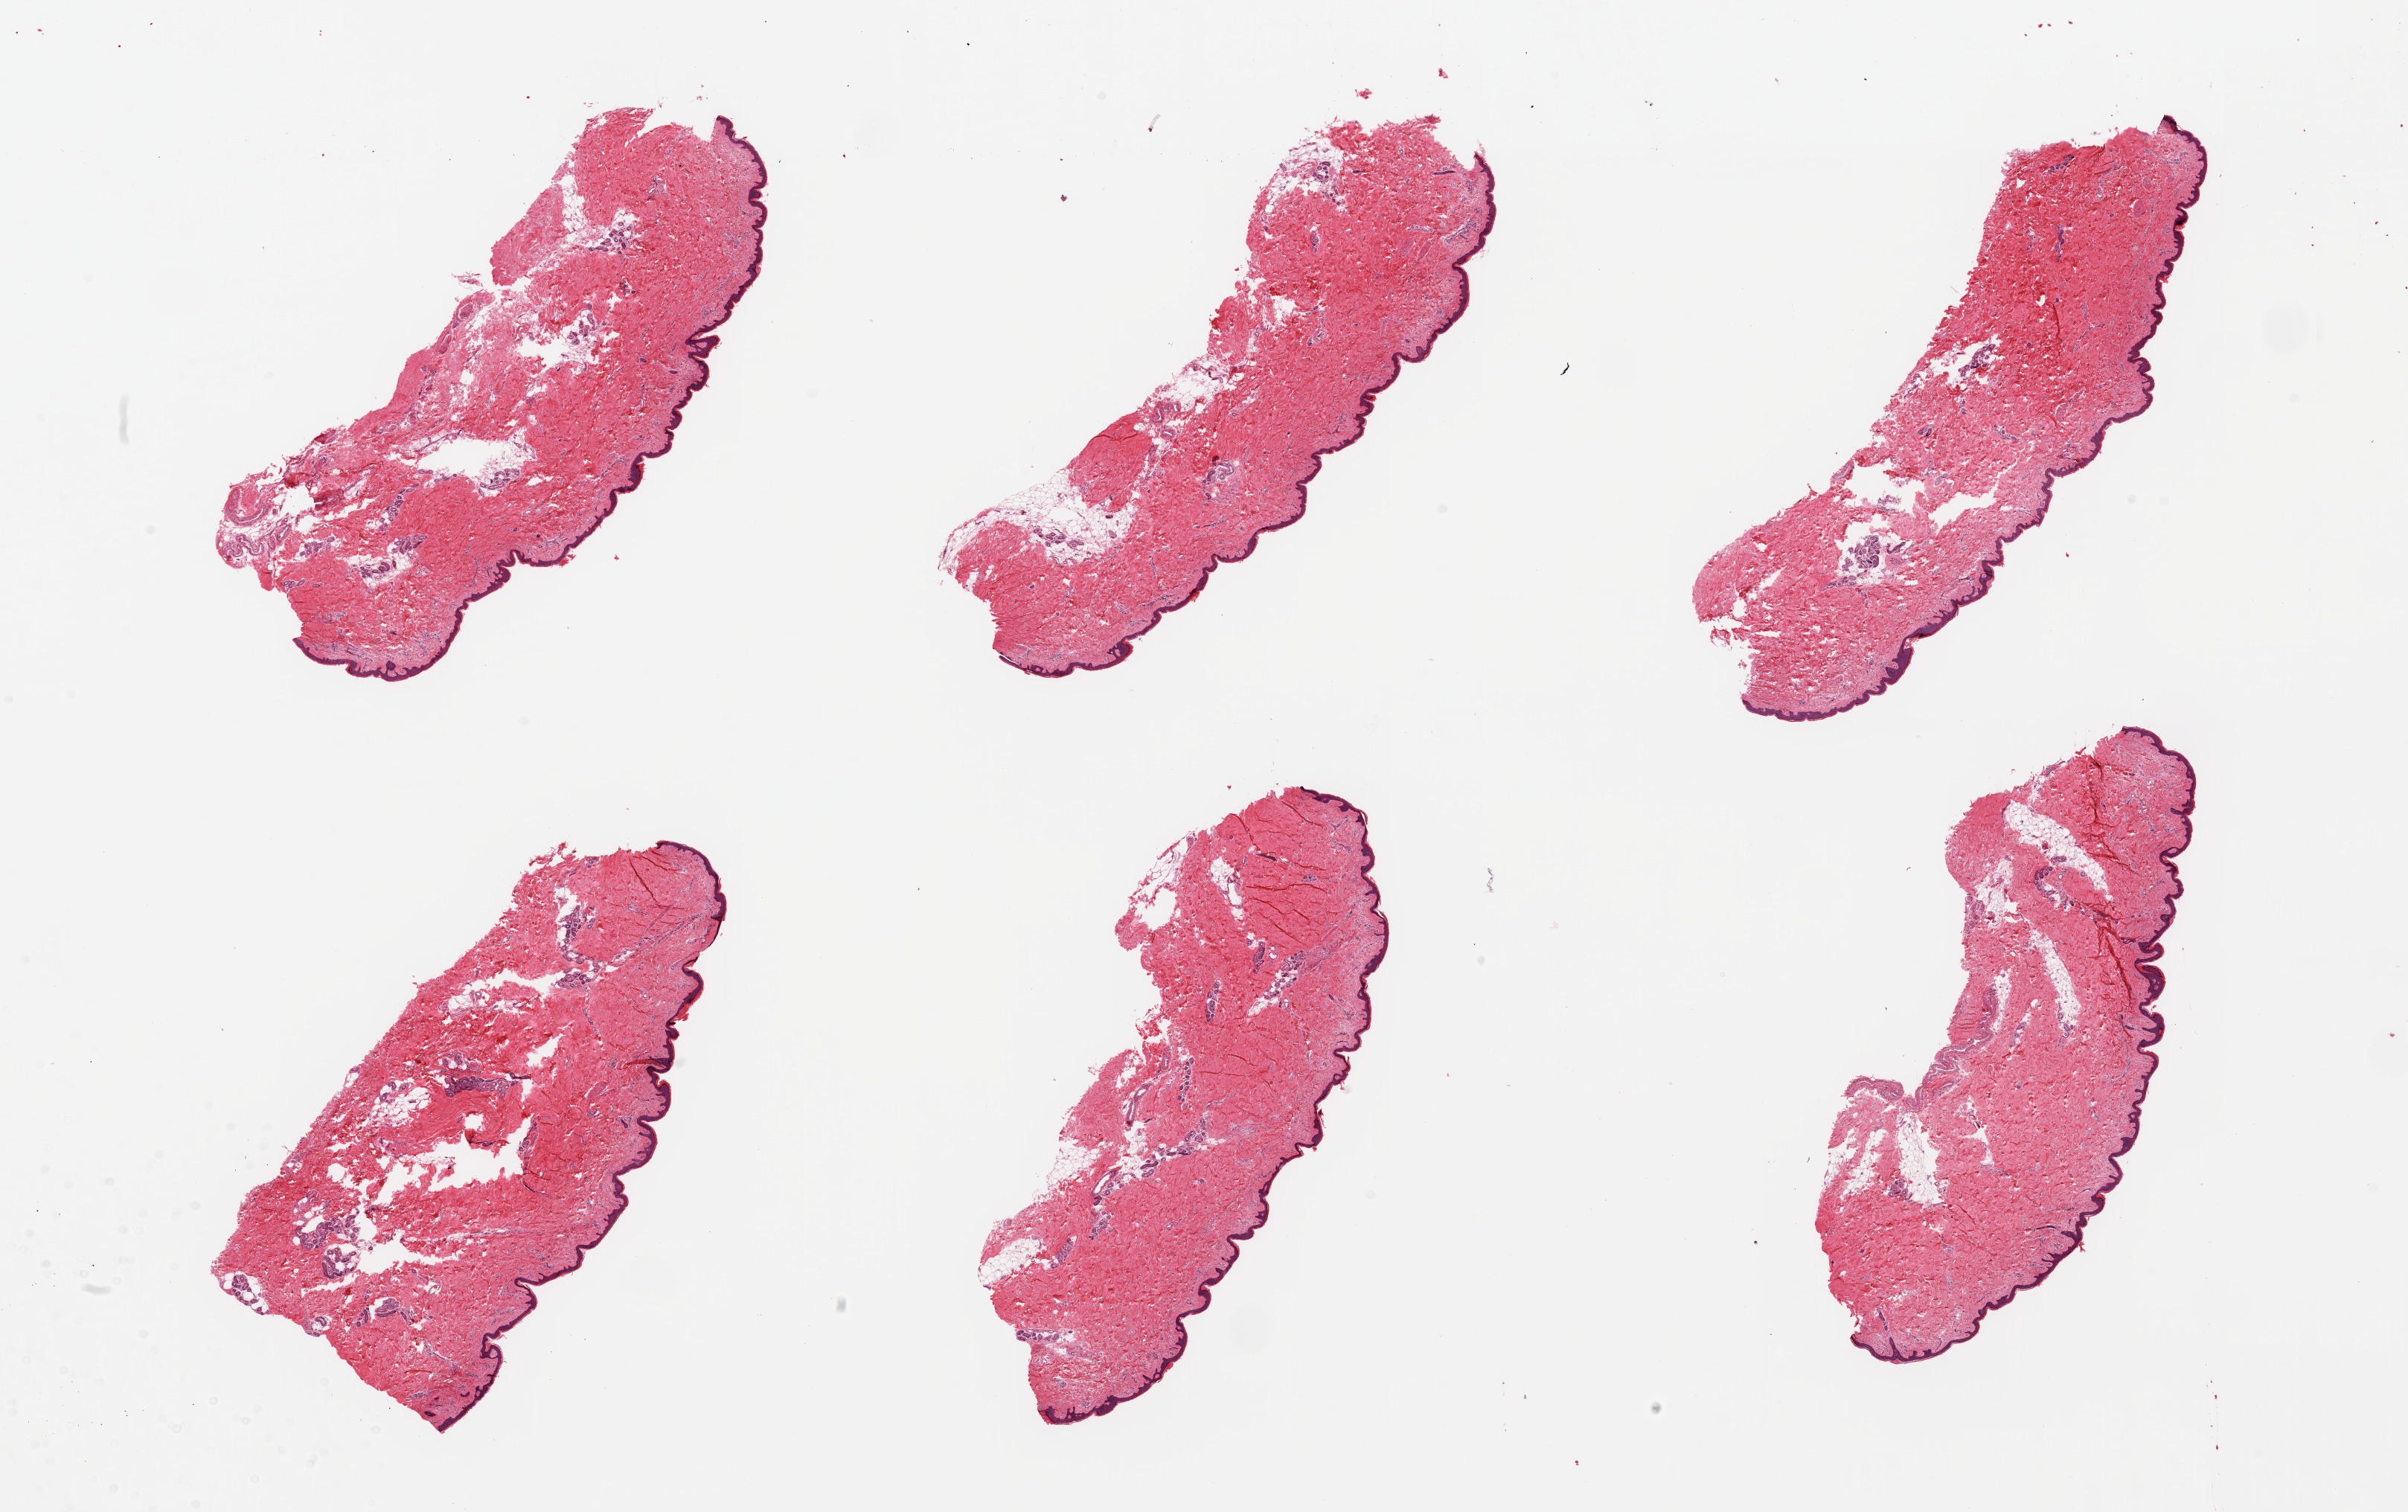
Digitized haematoxylin and eosin-stained section — low-resolution overview of the scanned area, about 25.6 x 16.1 mm (acquisition: 20x scan). PAXgene-fixed paraffin-embedded (PFPE) section. Section of skin of lower leg (target tissue). Donor tissue sample.
Reviewer comment on this tissue sample: 6 pieces, squamous epithelium is ~50-60 microns, trace adherent fat.